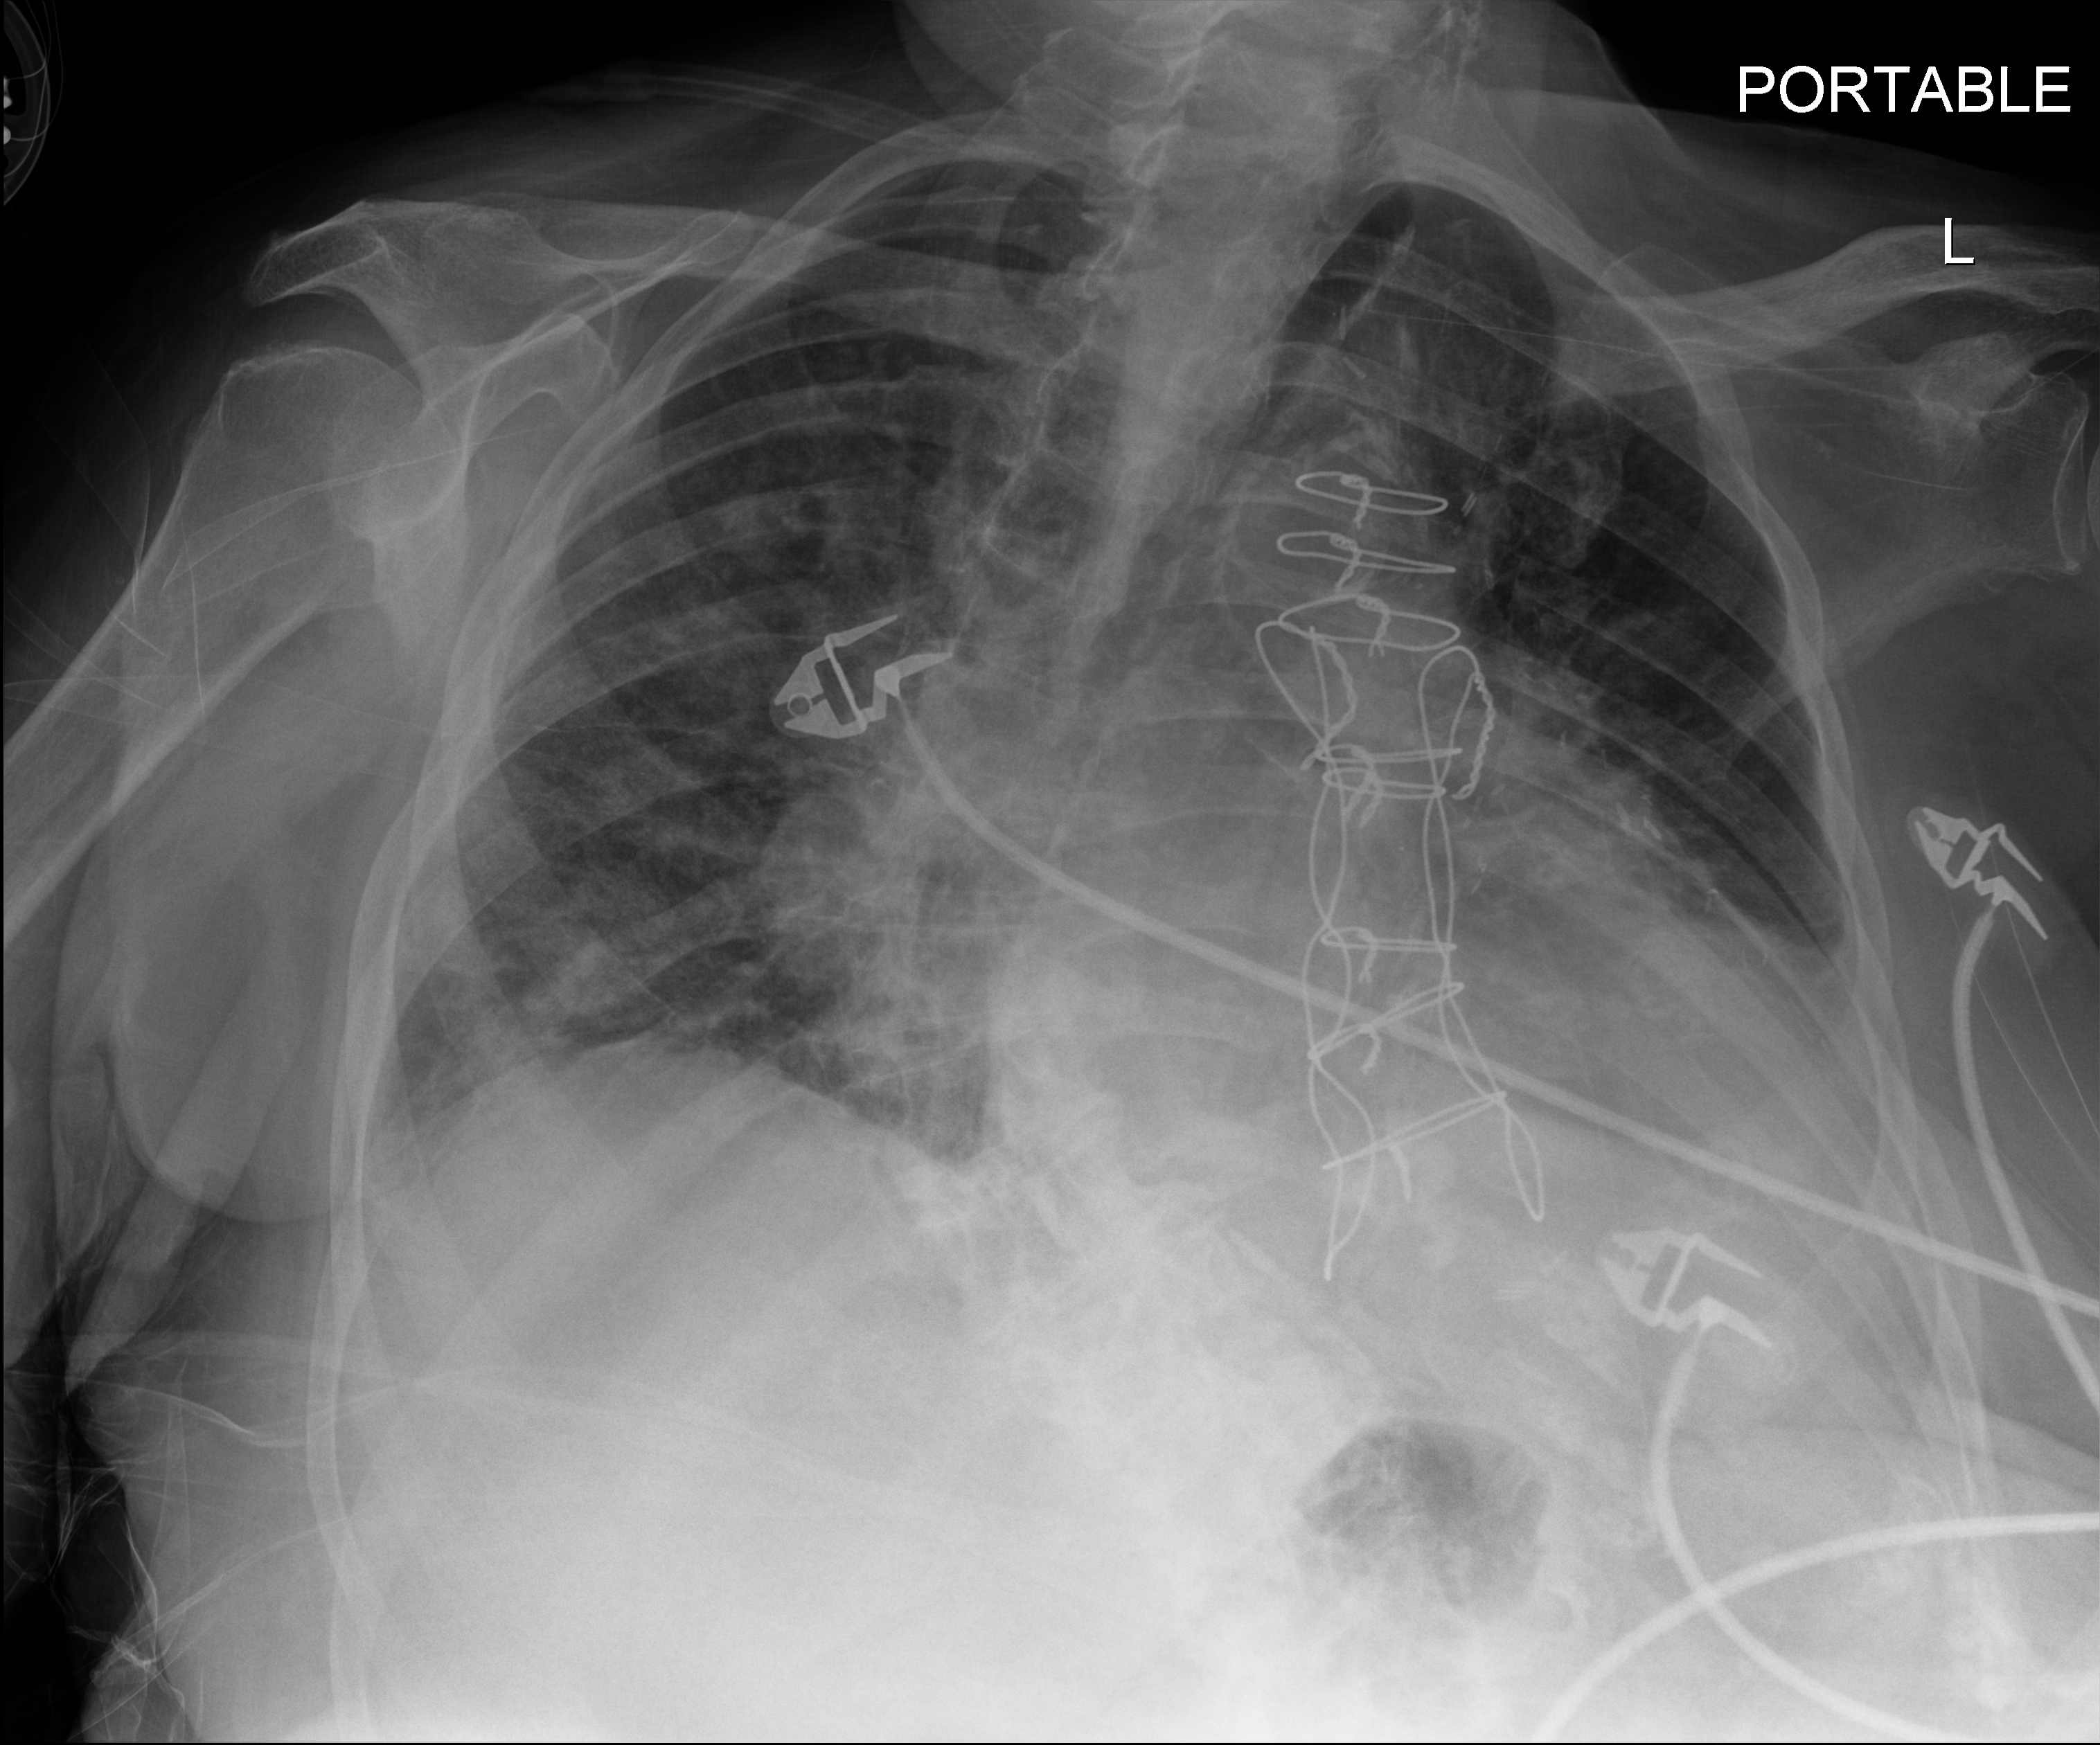
Chest X-ray (portable). Female patient hospitalised with COVID-19, age 75–90 years.
Admission-level facts for this patient (not findings on this image; timing relative to this image not recorded):
- length of hospital stay: 10 days
- admitted to intensive care during this hospital stay: no